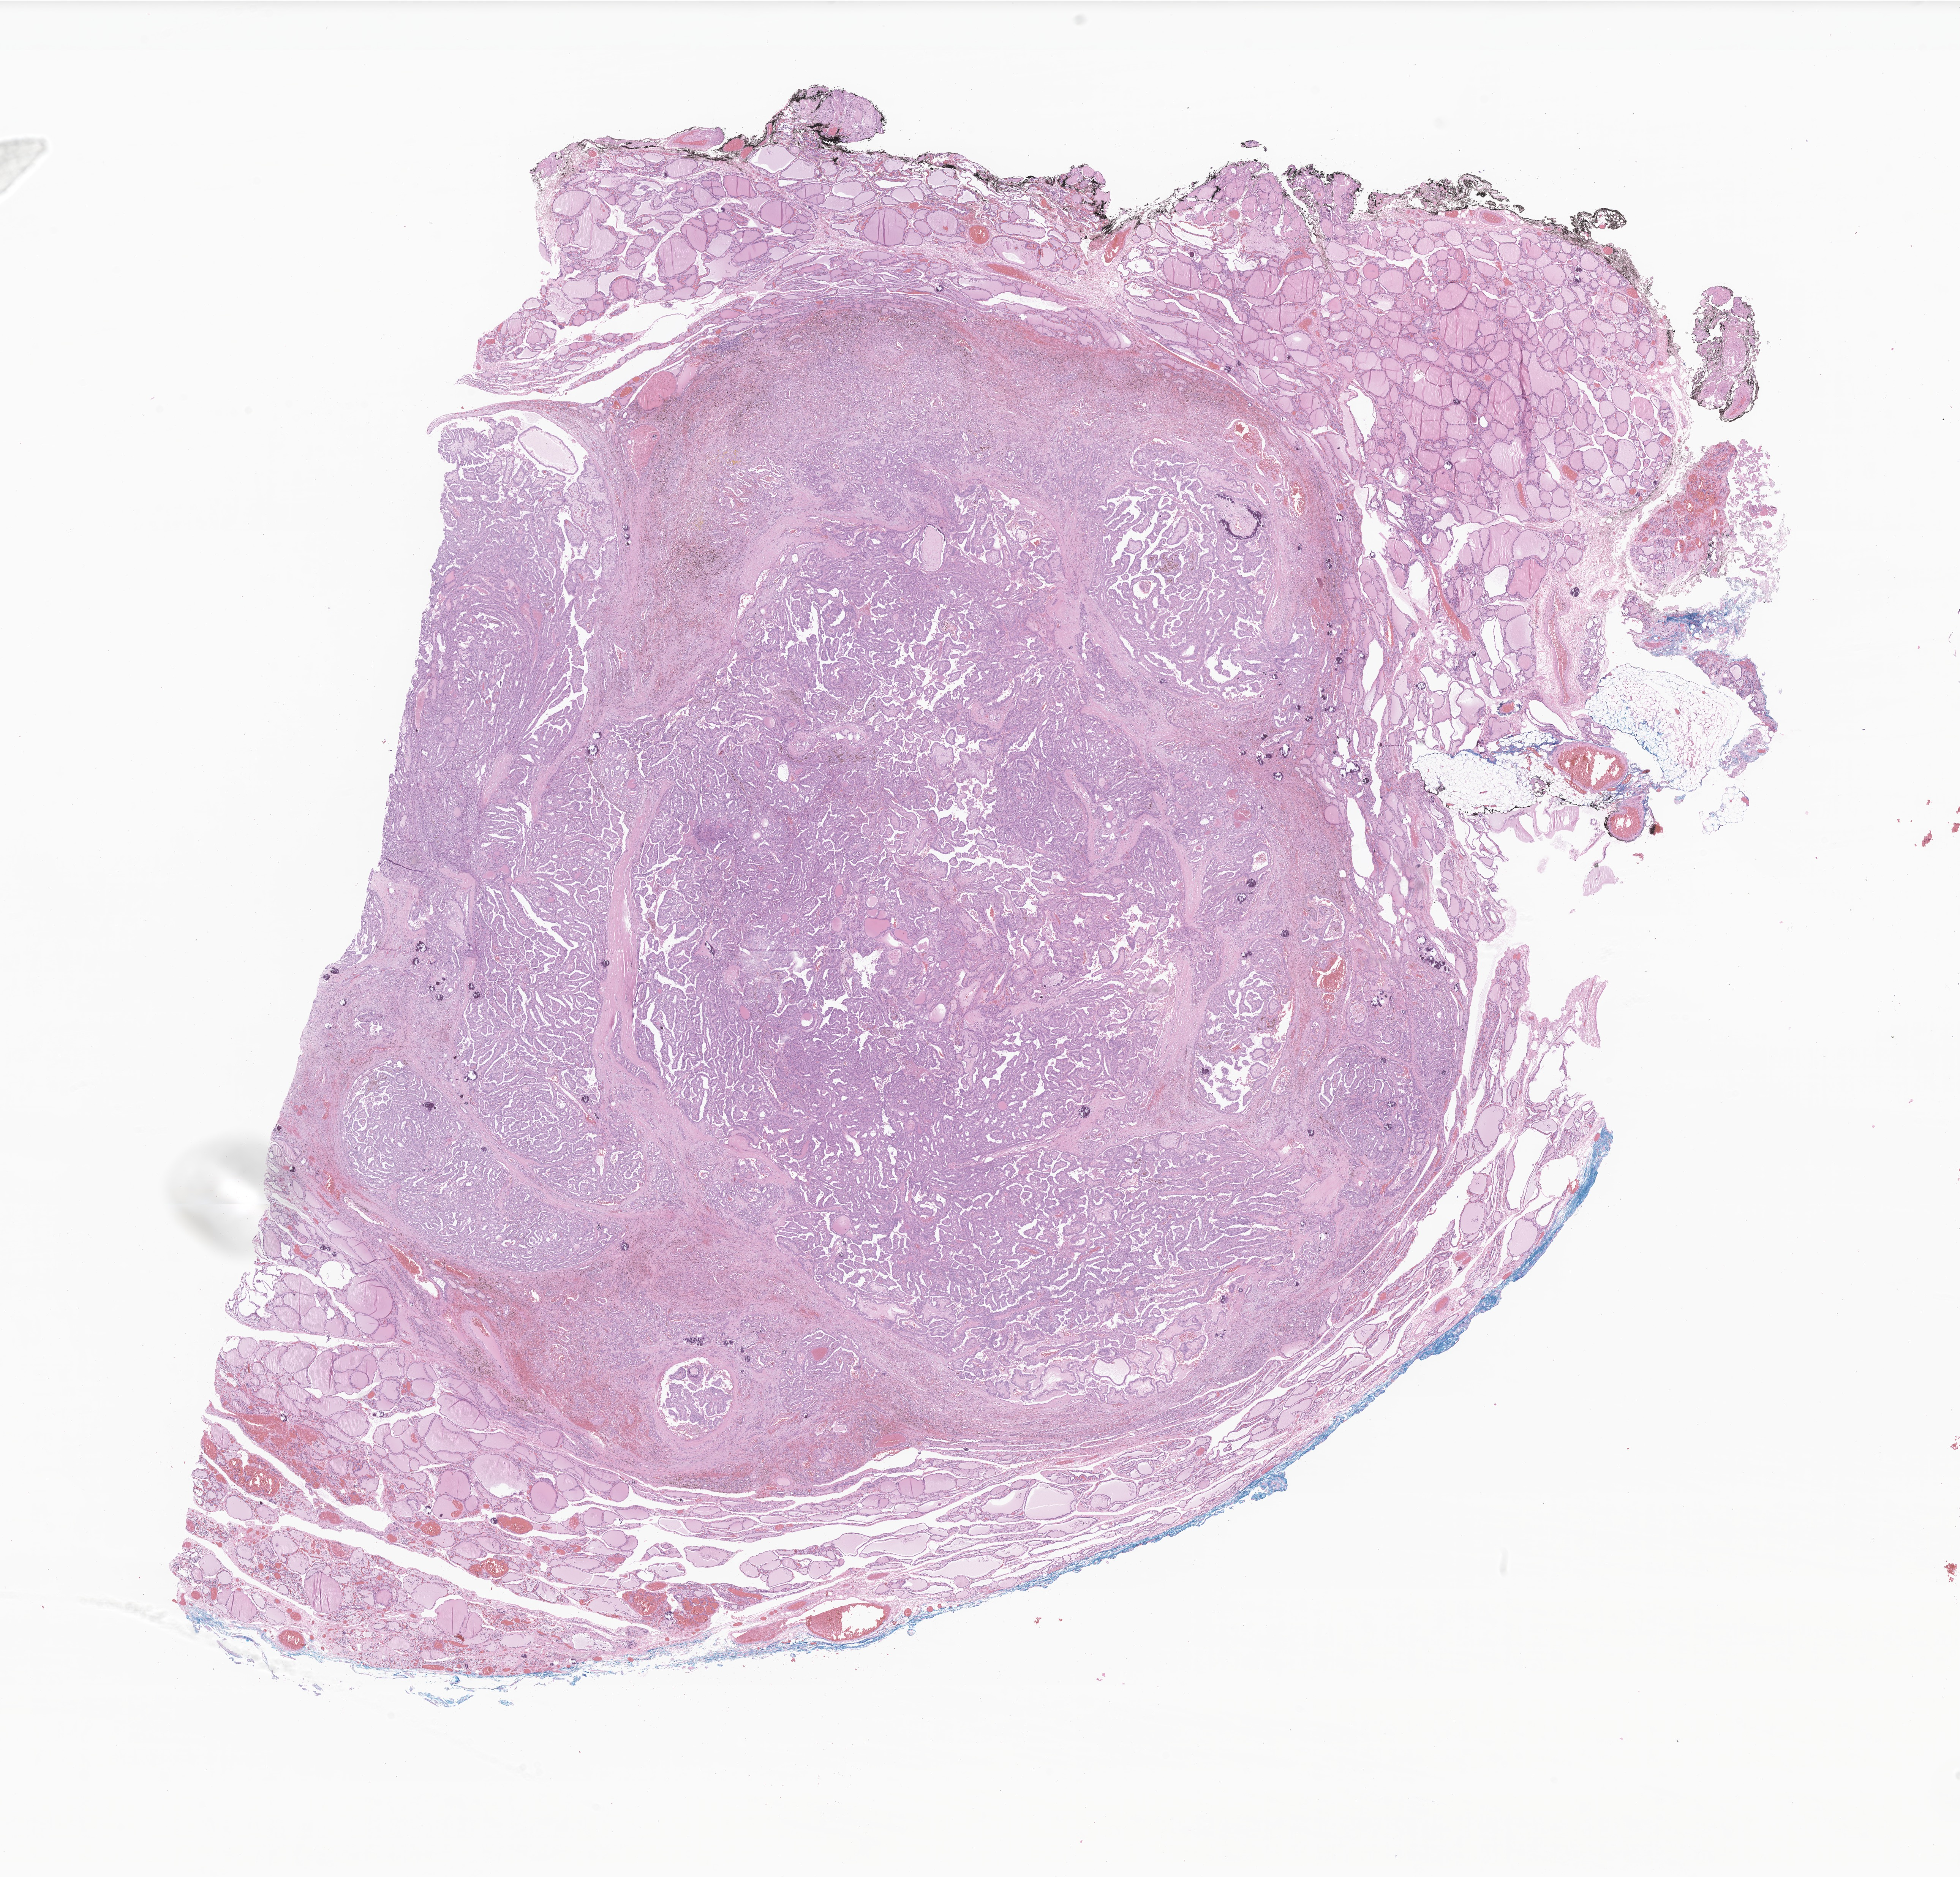
Whole-slide image, hematoxylin and eosin (H&E) stain of tumor tissue from the thyroid — shown as a low-resolution overview of the whole scanned area (about 21.8 x 20.8 mm); formalin-fixed paraffin-embedded section. Patient female; age 200 months (16 years 8 months).
- diagnosis (ICD-O-3 morphology term): Carcinoma, NOS